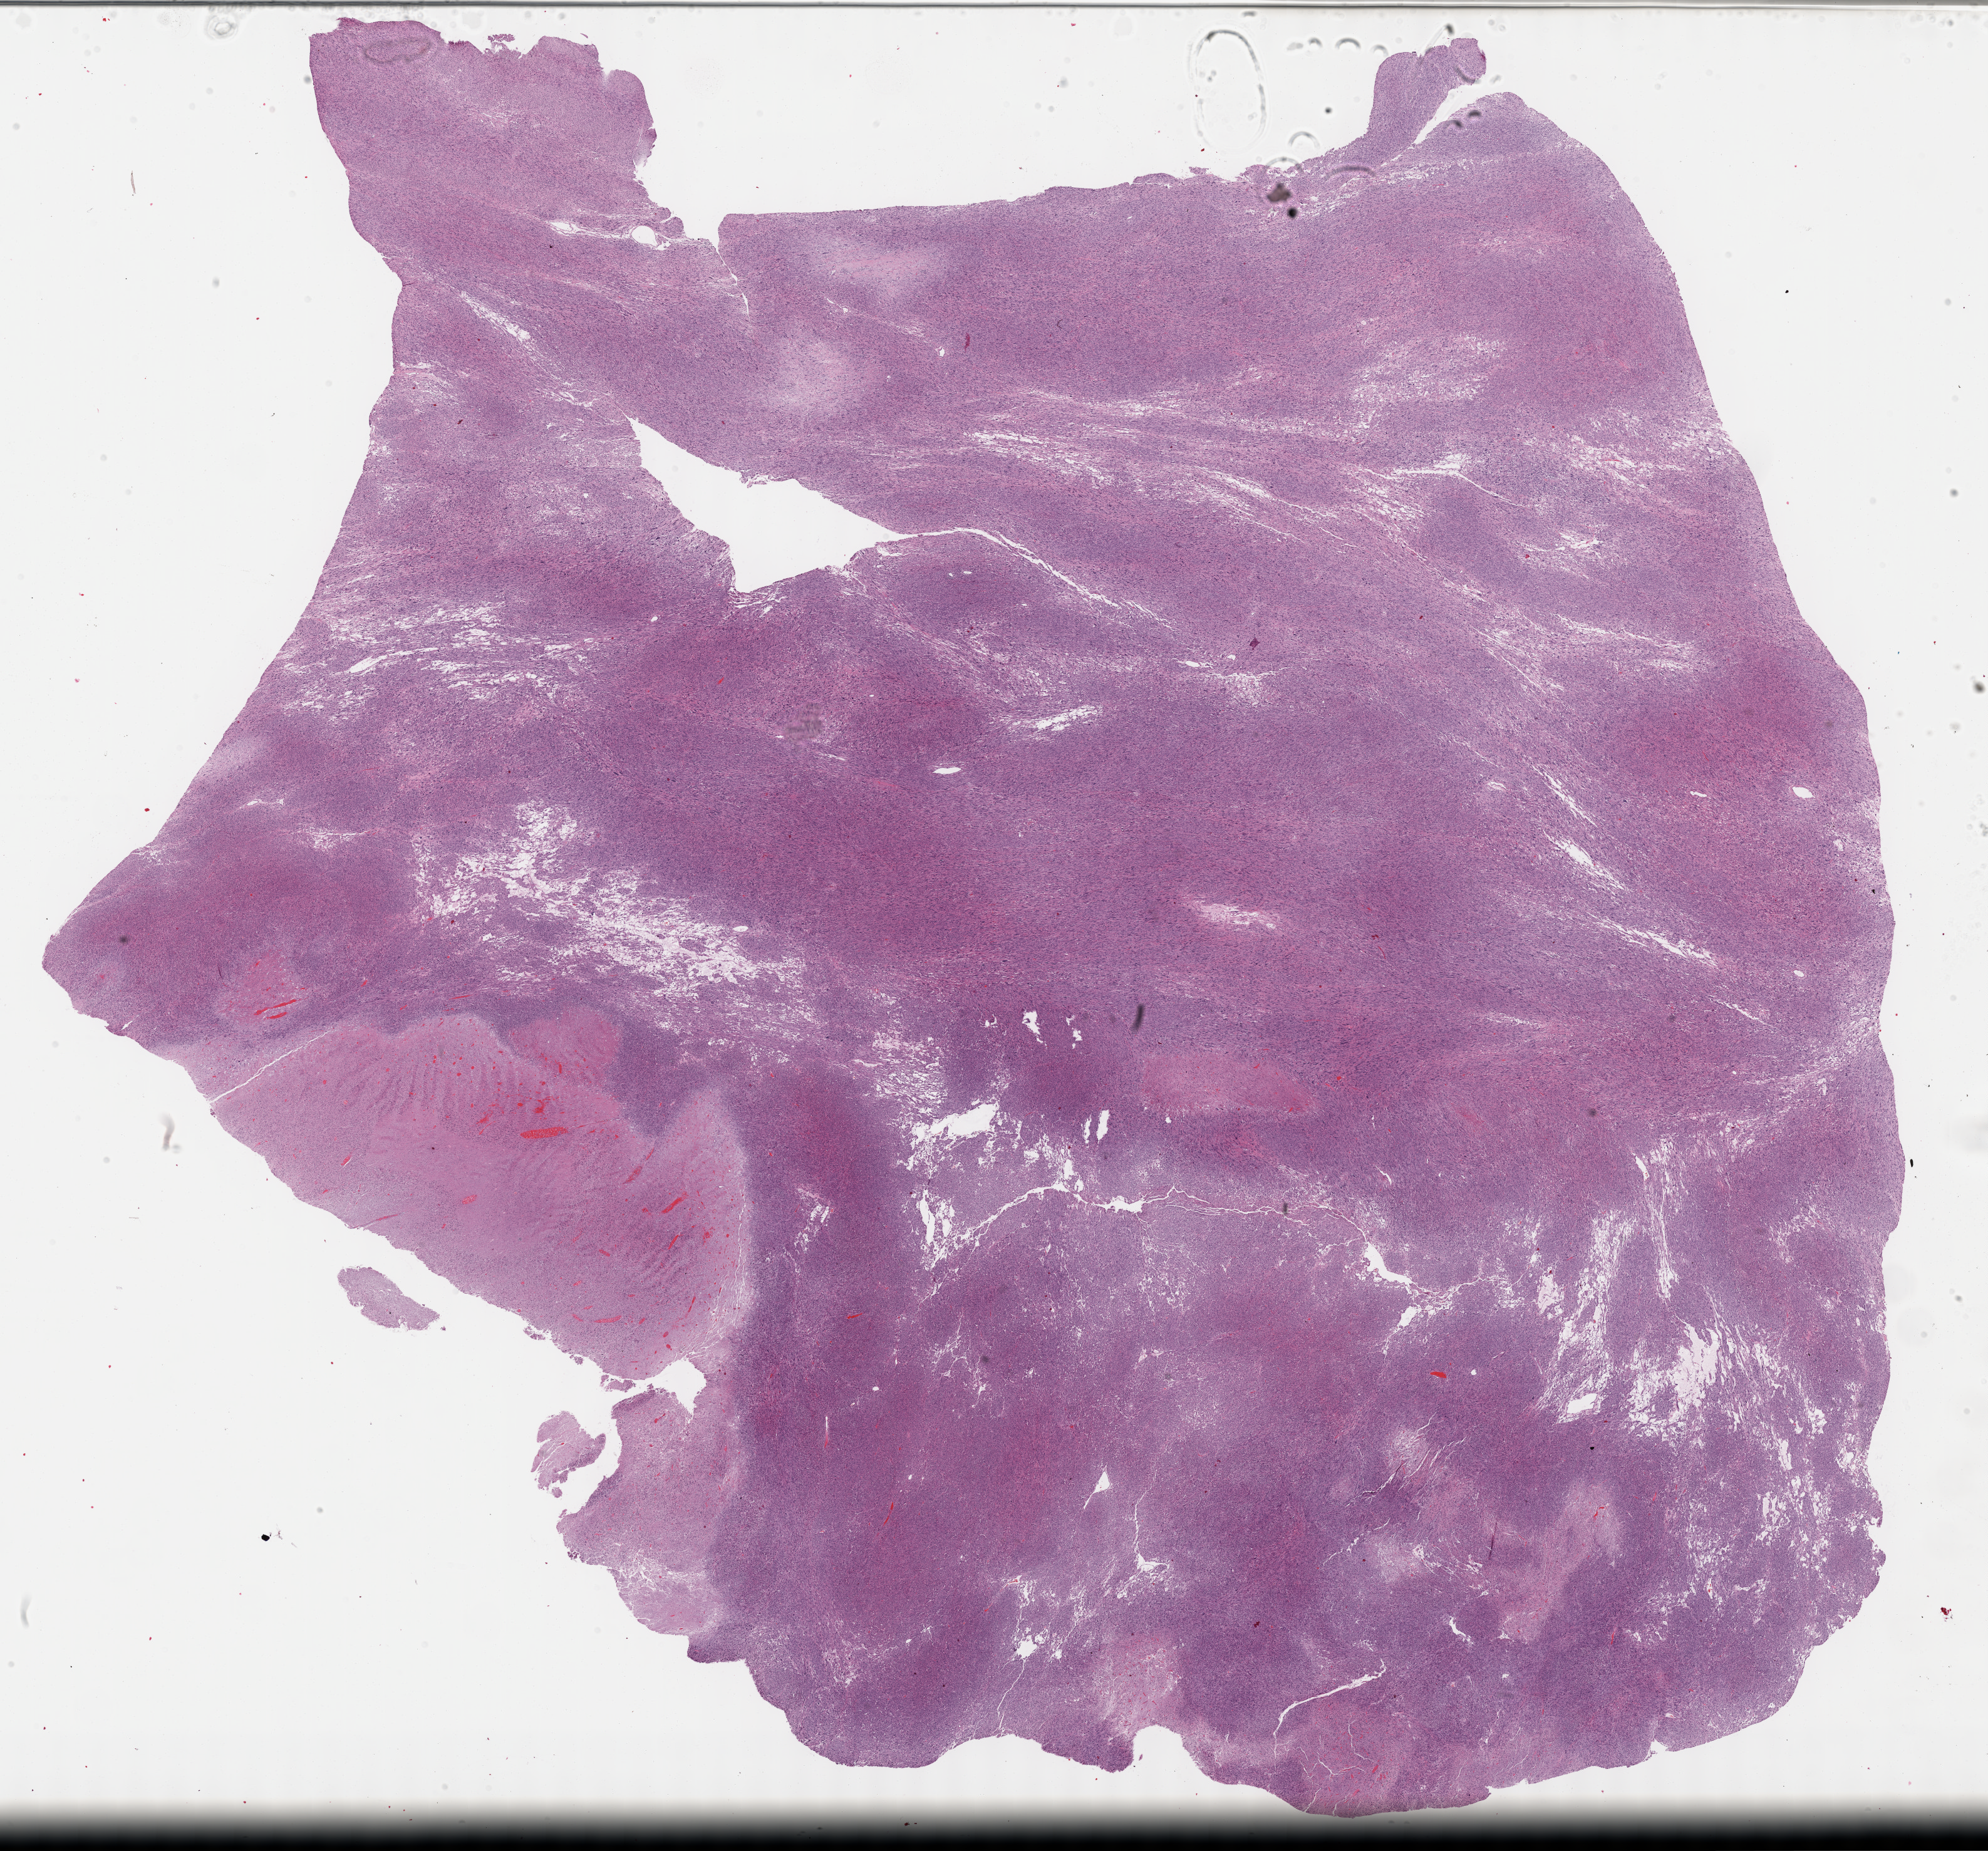
H&E whole-slide image, a low-resolution overview of the entire scanned area, about 25.7 x 23.9 mm, FFPE section, retroperitoneum and peritoneum, primary tumour sample. Female, age 63 years at initial diagnosis.
- pathologic diagnosis: Leiomyosarcoma, NOS (retroperitoneum)